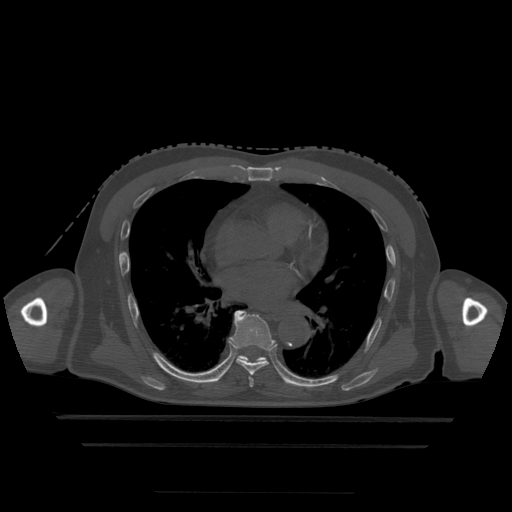
CT including the spine, one axial slice; position 295 of 522 along the scan axis; bone window (W 1800 / L 400 HU); 1.25 mm slice thickness; 512 × 512 image matrix, field of view 436 × 436 mm. Patient age 68 years. Case-level facts recorded for this patient, not image findings: primary cancer: urothelial.
Structures marked on this image (semi-automatically segmented with operator editing):
- T6 vertebra: box from (x=249, y=378) to (x=254, y=388) px
- T7 vertebra: (x=230, y=311)–(x=276, y=376)
- T8 vertebra: (x=237, y=356)–(x=267, y=363)